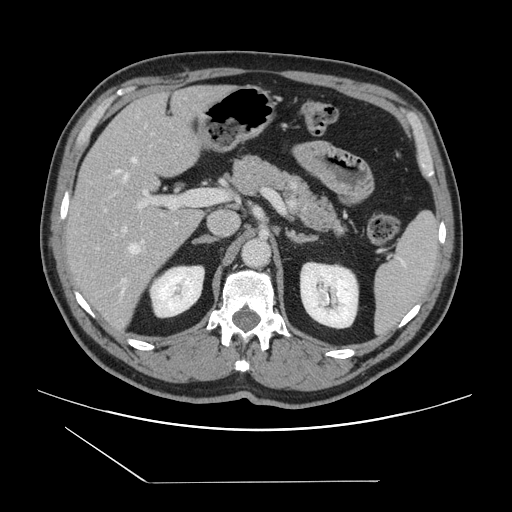
Contrast-enhanced abdominal CT, one axial slice. Slice 83 of 157 in the series (ordered by position). Intravenous contrast given. Soft-tissue window (W 400 / L 40 HU). 2.5 mm slice thickness. 512 × 512 image matrix, field of view 407 × 407 mm. Male patient, age 61 years. Case-level facts recorded for this patient, not image findings: diagnosis: colorectal cancer liver metastases, imaged before liver resection; multiple liver metastases: yes; largest metastasis: 5.5 cm; chemotherapy before resection: no.
Structures marked on this image (expert manual segmentation):
- hepatic veins: box from (x=115, y=157) to (x=143, y=292) px
- liver: (x=66, y=86)–(x=227, y=335)
- planned liver remnant (the part of the liver to remain after resection): (x=67, y=86)–(x=226, y=221)
- portal vein (with intrahepatic branches): (x=105, y=189)–(x=206, y=232)